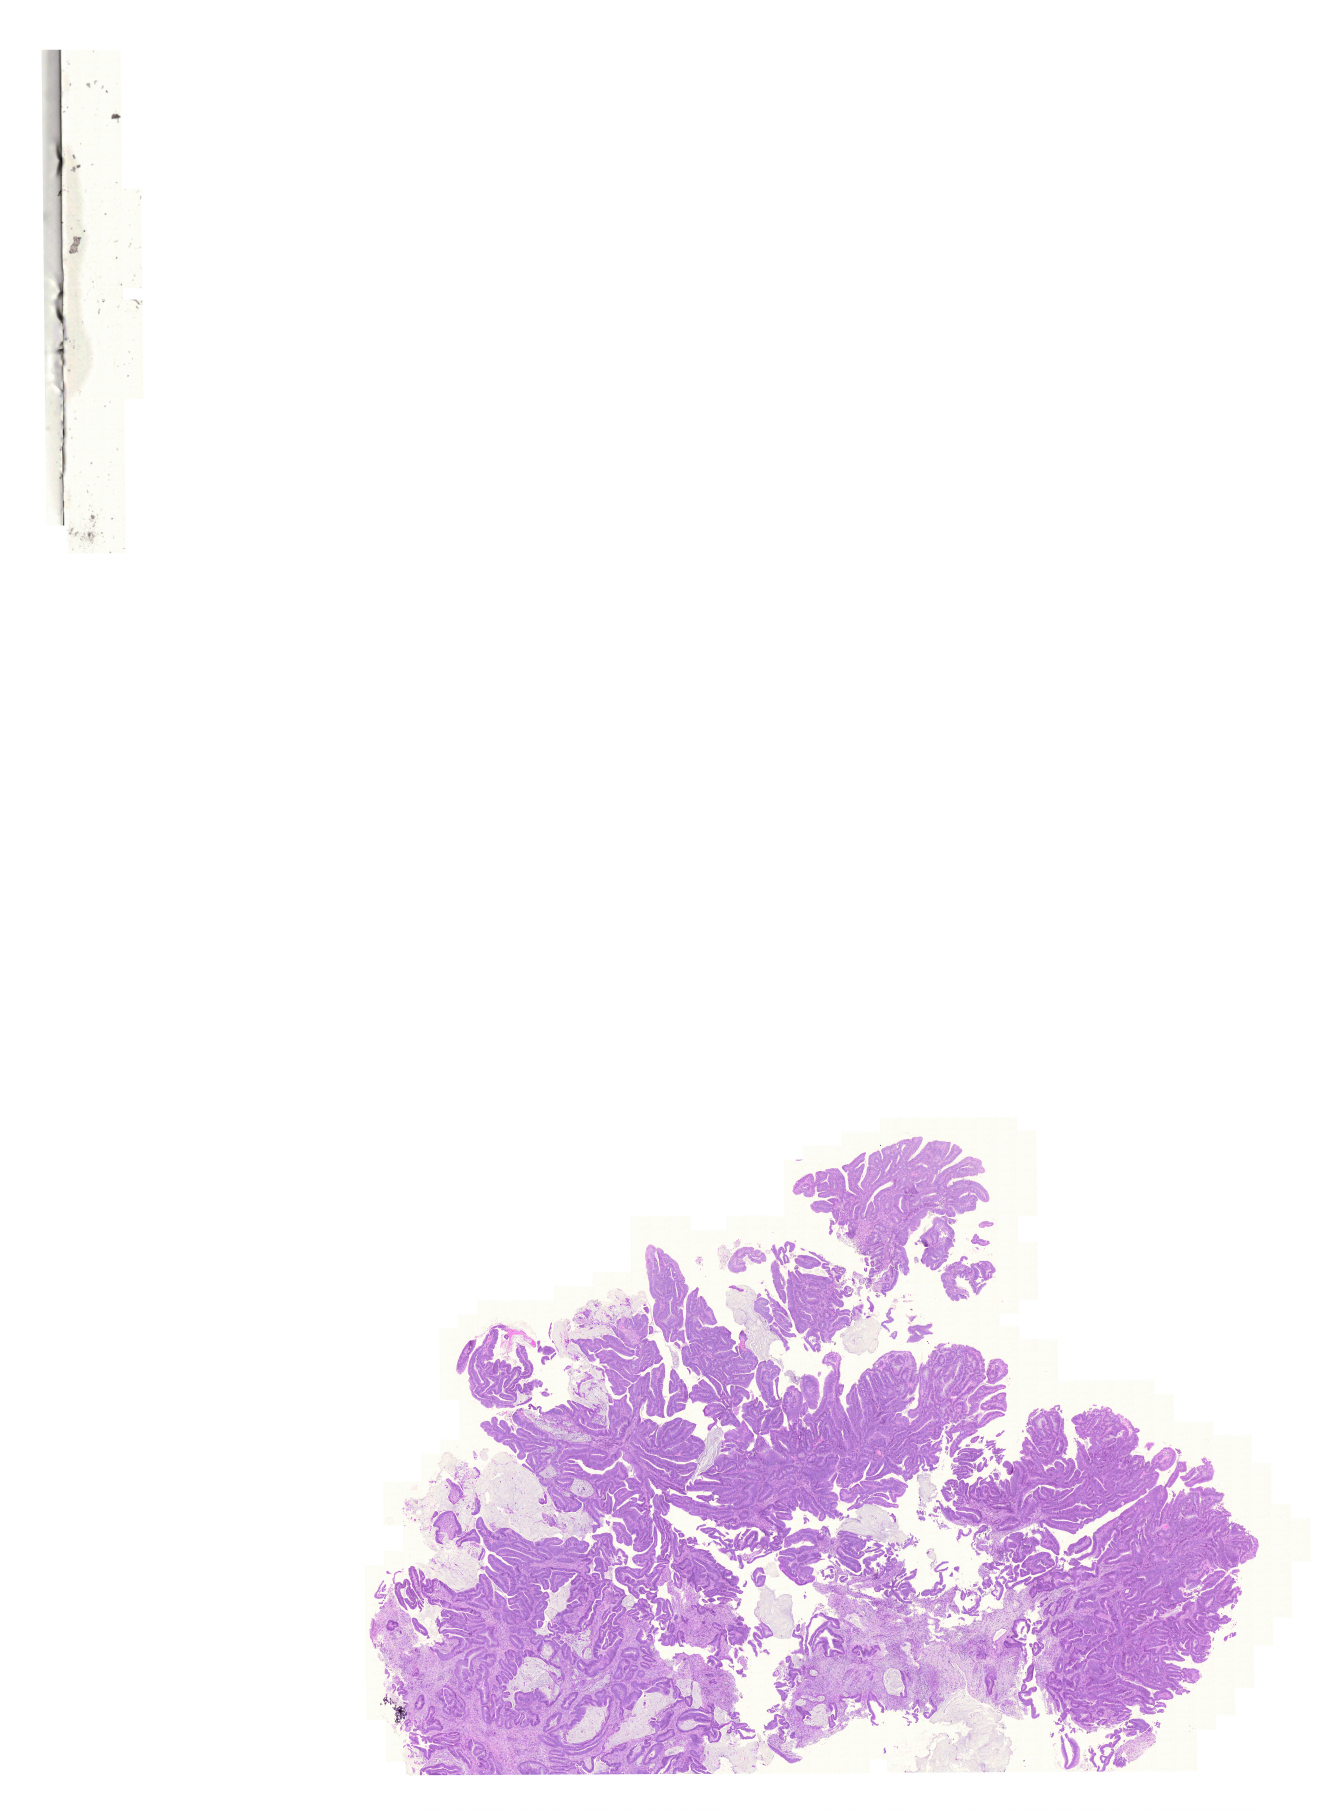
Whole-slide histology image, H&E-stained — shown as a low-resolution overview of the whole scanned area (about 19.9 x 27.0 mm); formalin-fixed paraffin-embedded (FFPE) diagnostic section; primary tumour sample from the colon. Patient: male, age at initial diagnosis 82 years.
• diagnosis: Adenocarcinoma, NOS (transverse colon)
• lymph nodes positive (case pathology): 0 of 18 examined
• AJCC pathologic stage: II (6th edition)